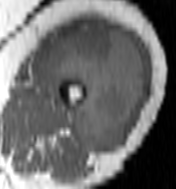
MRI of an extremity soft-tissue mass, one axial slice; position 61 of 100 along the scan axis; MR volume resampled by the dataset authors to the PET/CT grid (not the native acquisition matrix); 3.27 mm slice thickness; 176 × 189 image matrix, field of view 172 × 185 mm. Female patient. From the clinical record (not read from this slice): histological type: undifferentiated – high grade; grade: high; site of the primary tumour: left thigh.
Annotated regions visible in this slice (expert contour drawn on MRI and transferred to this co-registered scan by the dataset authors):
- gross tumour volume including surrounding oedema: box from (x=46, y=23) to (x=145, y=152) px
- gross tumour volume (mass): (x=46, y=23)–(x=145, y=152)